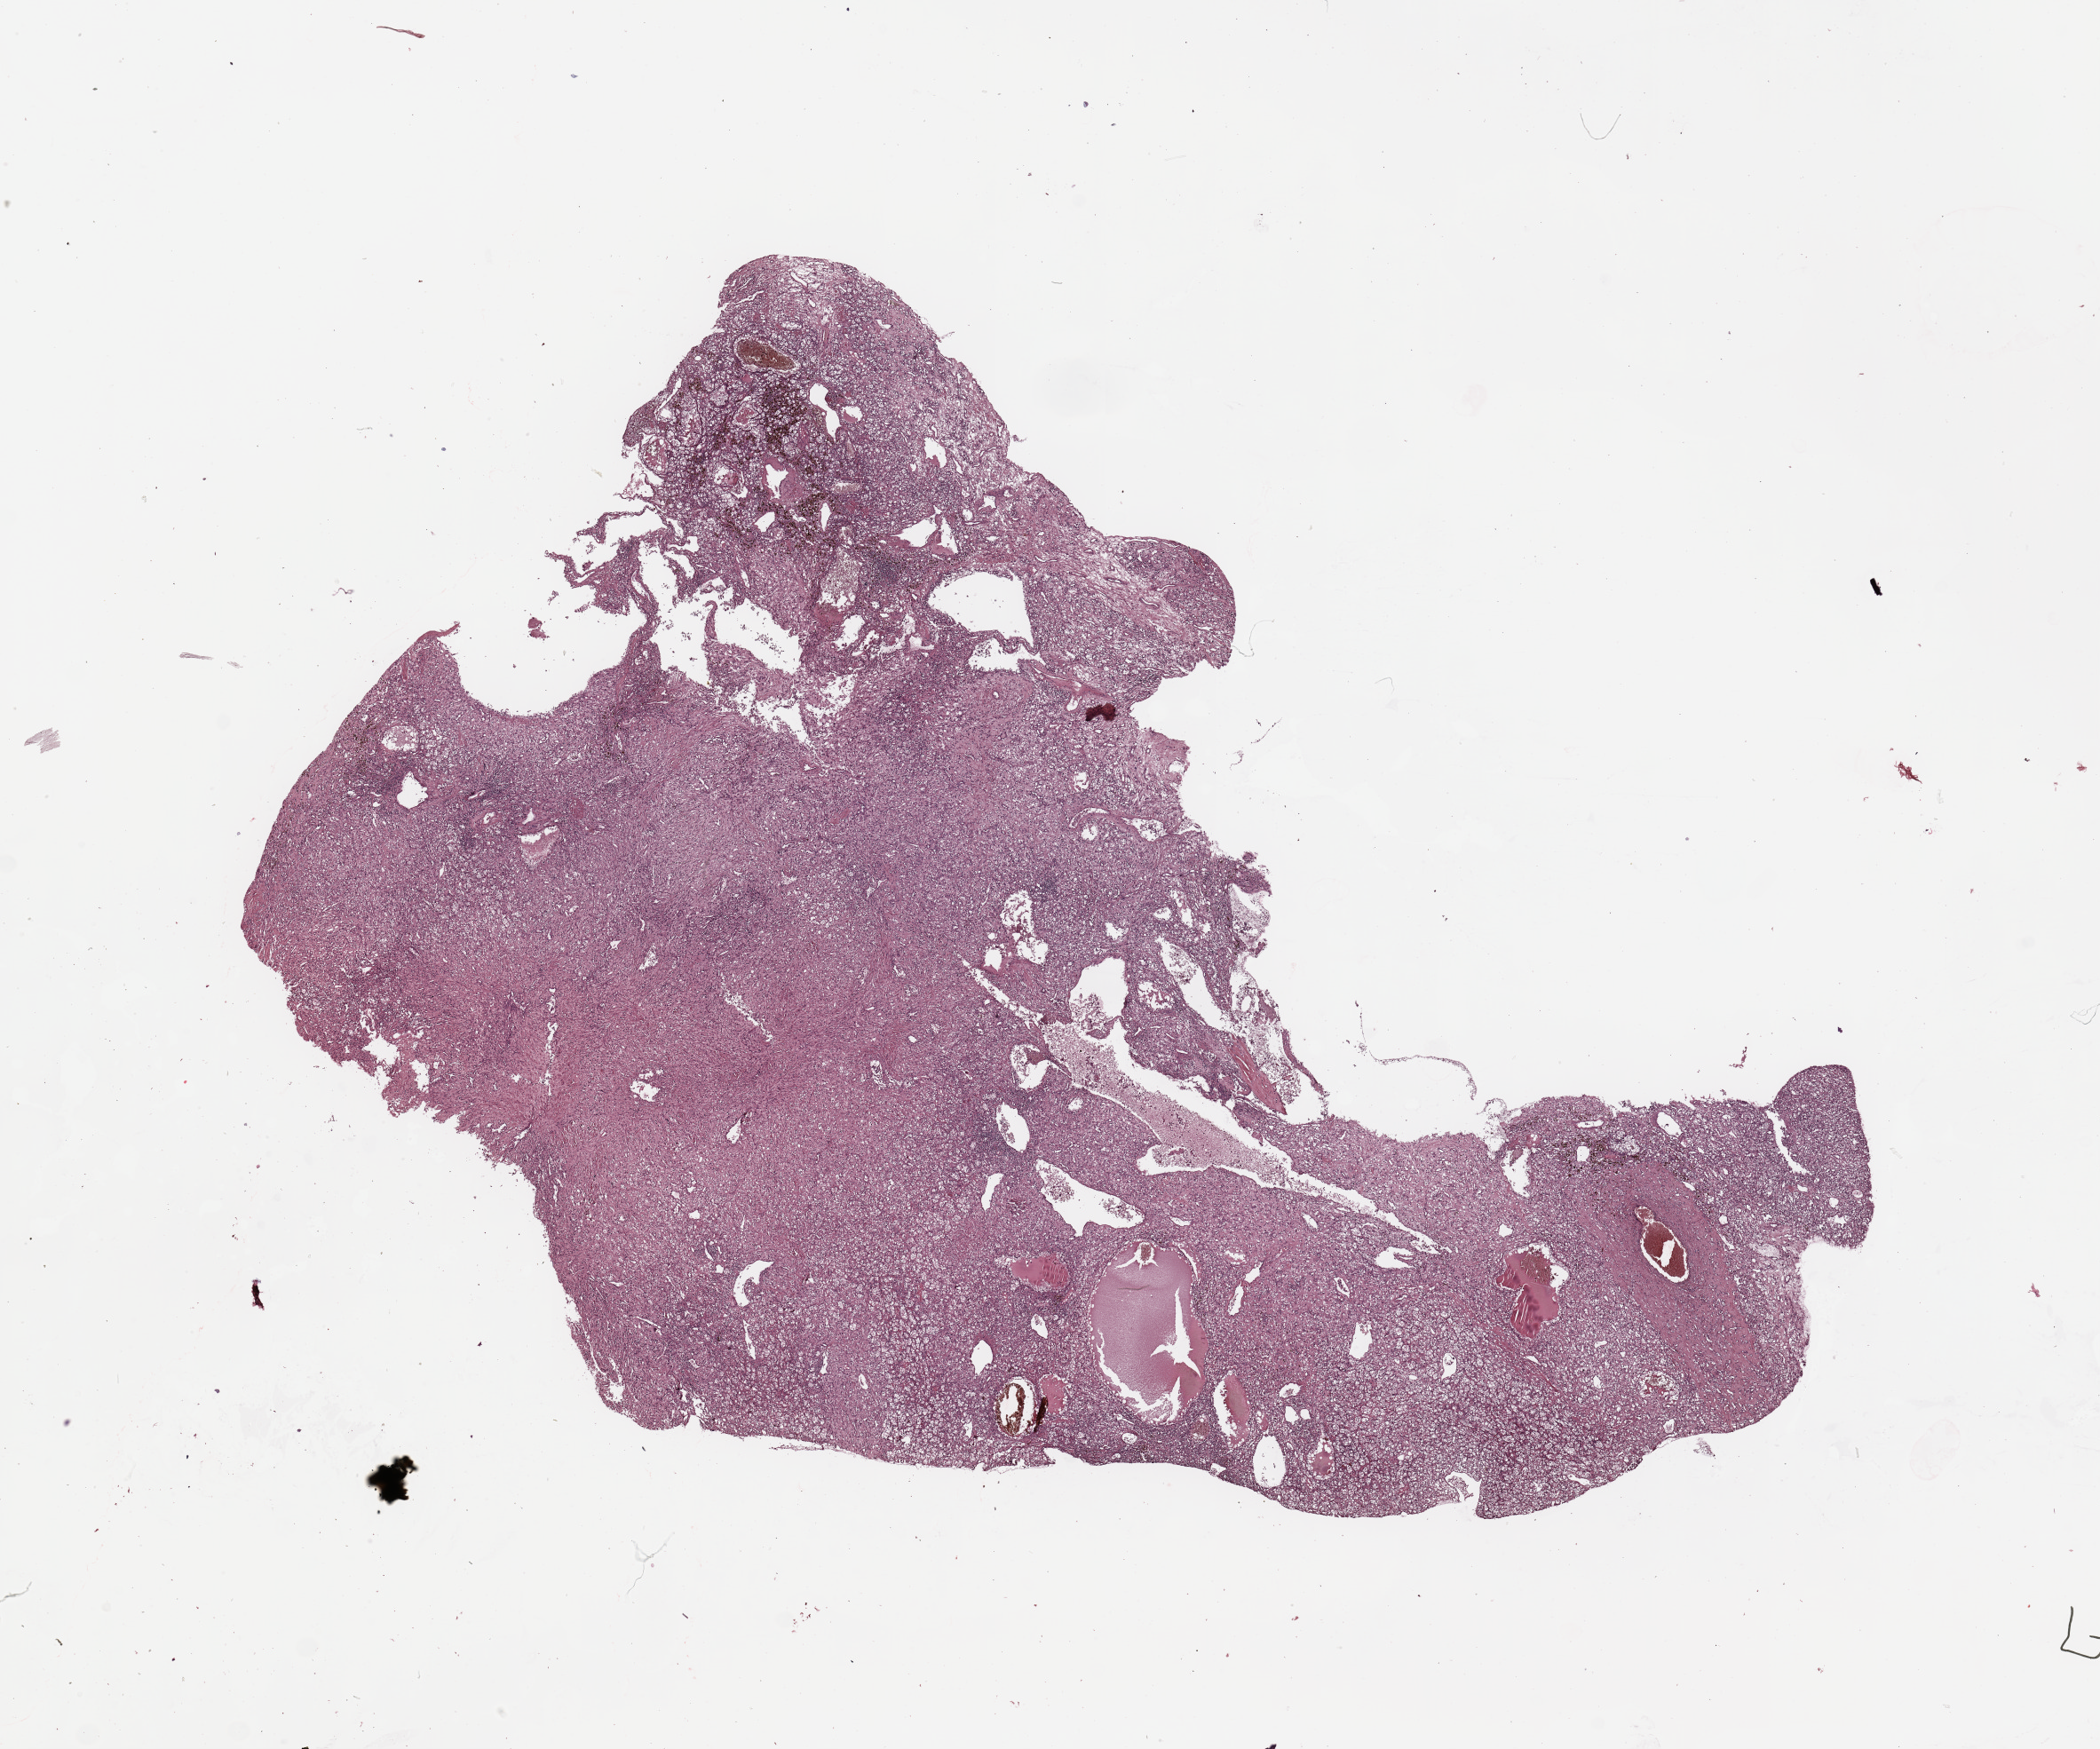
Digitized Hematoxylin and eosin (H&E) stained tissue section (whole slide) — low-resolution overview of the scanned area, about 18.7 x 15.6 mm (from a 20x scan); tumour tissue sample, sampled site: kidney. Patient: male, age 51 years. Histologic grade: G4 (undifferentiated). Slide review estimates, as recorded: tumour nuclei 90%, necrosis 10%.
Primary tumour site (as recorded): middle. AJCC pathologic stage: IV. Histologic diagnosis: Renal cell carcinoma, NOS.